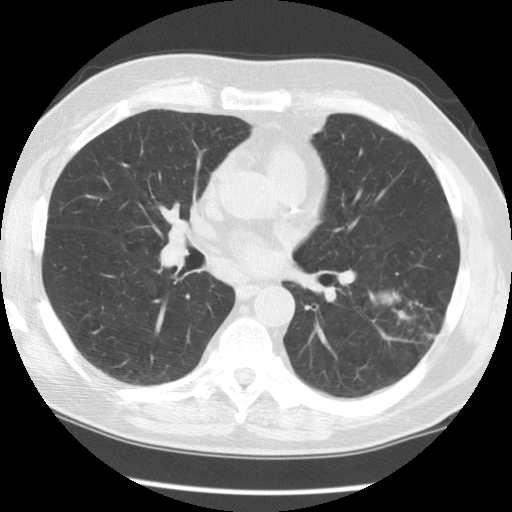
Low-dose screening chest CT, one axial slice; position 71 of 130 along the scan axis; reconstruction kernel STANDARD; 120 kVp; lung window (W 1500 / L -600 HU); 512 × 512 image matrix.
Outlined on this slice (outlined manually by an expert reader):
- lesion 1 (tumor, lower lobe of left lung): box from (x=377, y=292) to (x=401, y=305) px